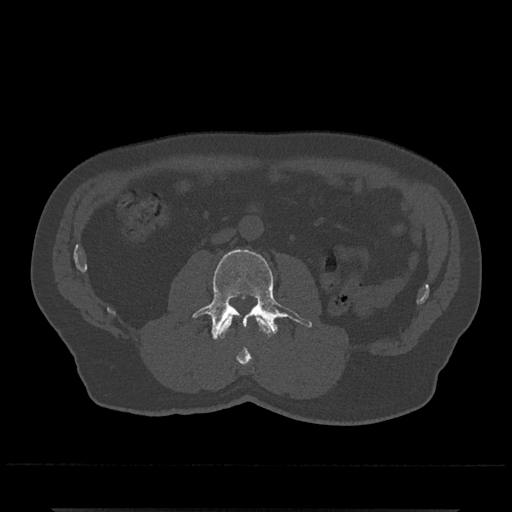
CT including the spine, one axial slice; position 236 of 797 along the scan axis; bone window (W 1800 / L 400 HU); 0.5 mm slice thickness; 512 × 512 image matrix, field of view 393 × 393 mm. Patient: male, 67 years. From the clinical record (not read from this slice): primary cancer: prostate.
Annotated regions visible in this slice (semi-automatically segmented with operator editing):
- L2 vertebra: bounding box [x1, y1, x2, y2] px = [218, 315, 271, 365]
- L3 vertebra: [192, 249, 313, 340]